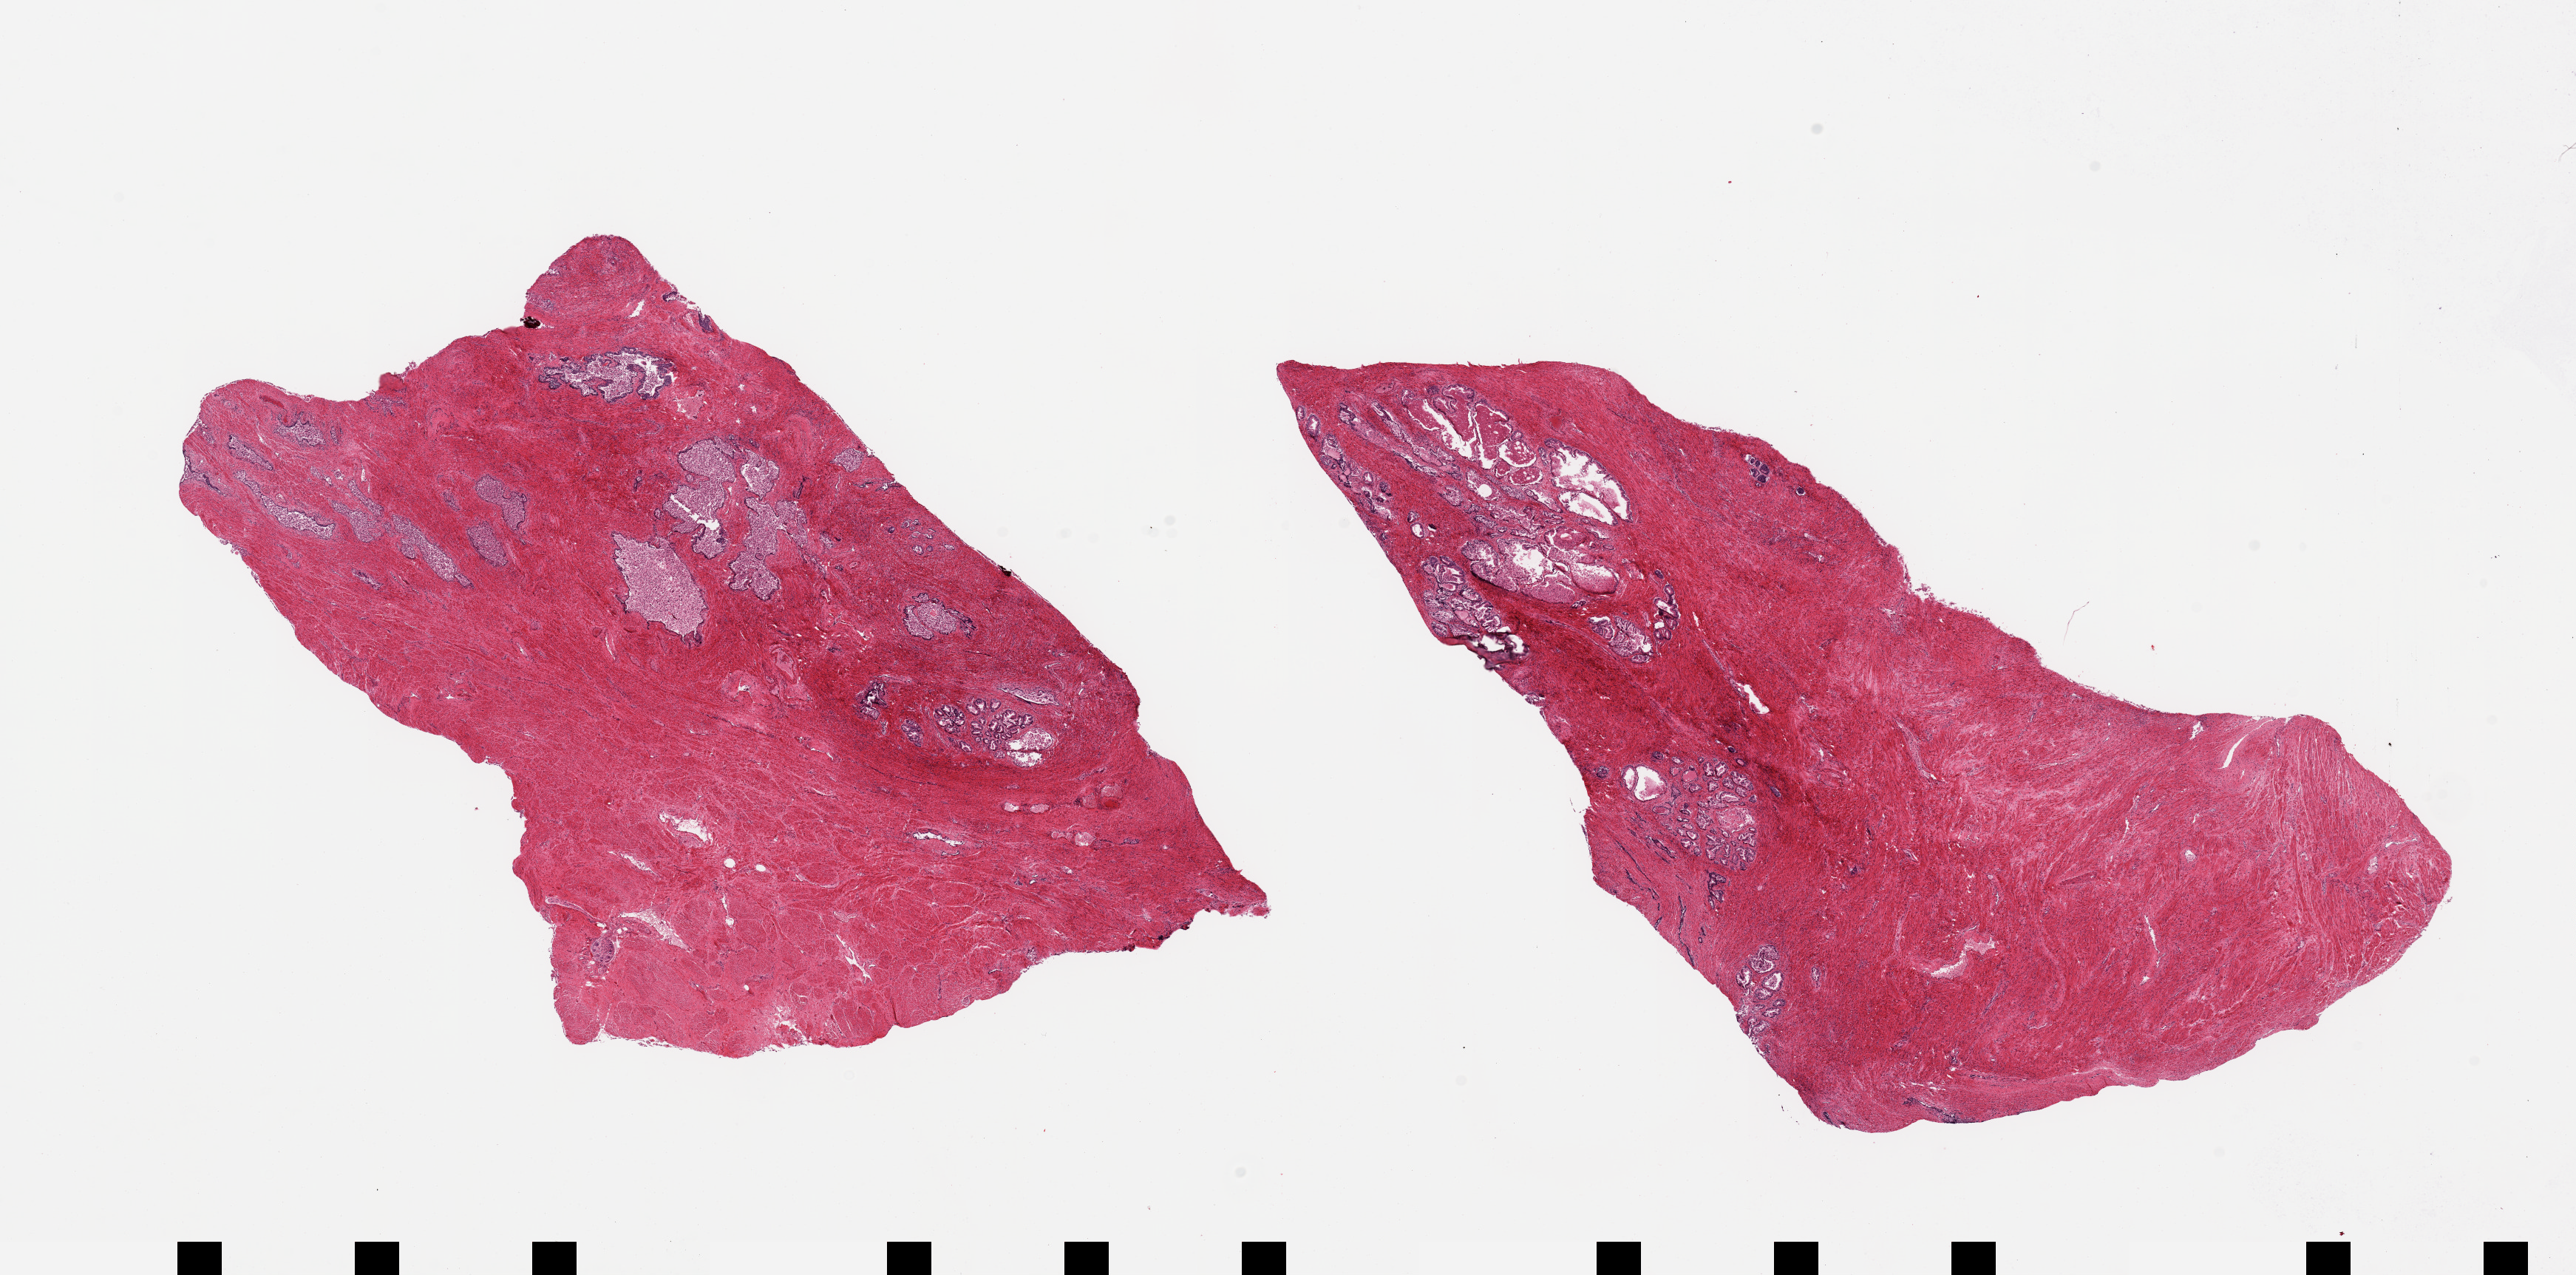
Whole-slide image, hematoxylin and eosin (H&E) stain, low-resolution overview of the scanned area, about 27.6 x 13.6 mm (from a 20x scan); PAXgene-fixed paraffin-embedded (PFPE) section; sampled site (target tissue): prostate; donor tissue sample.
Reviewer comment on this tissue sample: 2 pieces; each piece is ~50% stroma, 50% stroma and glands.